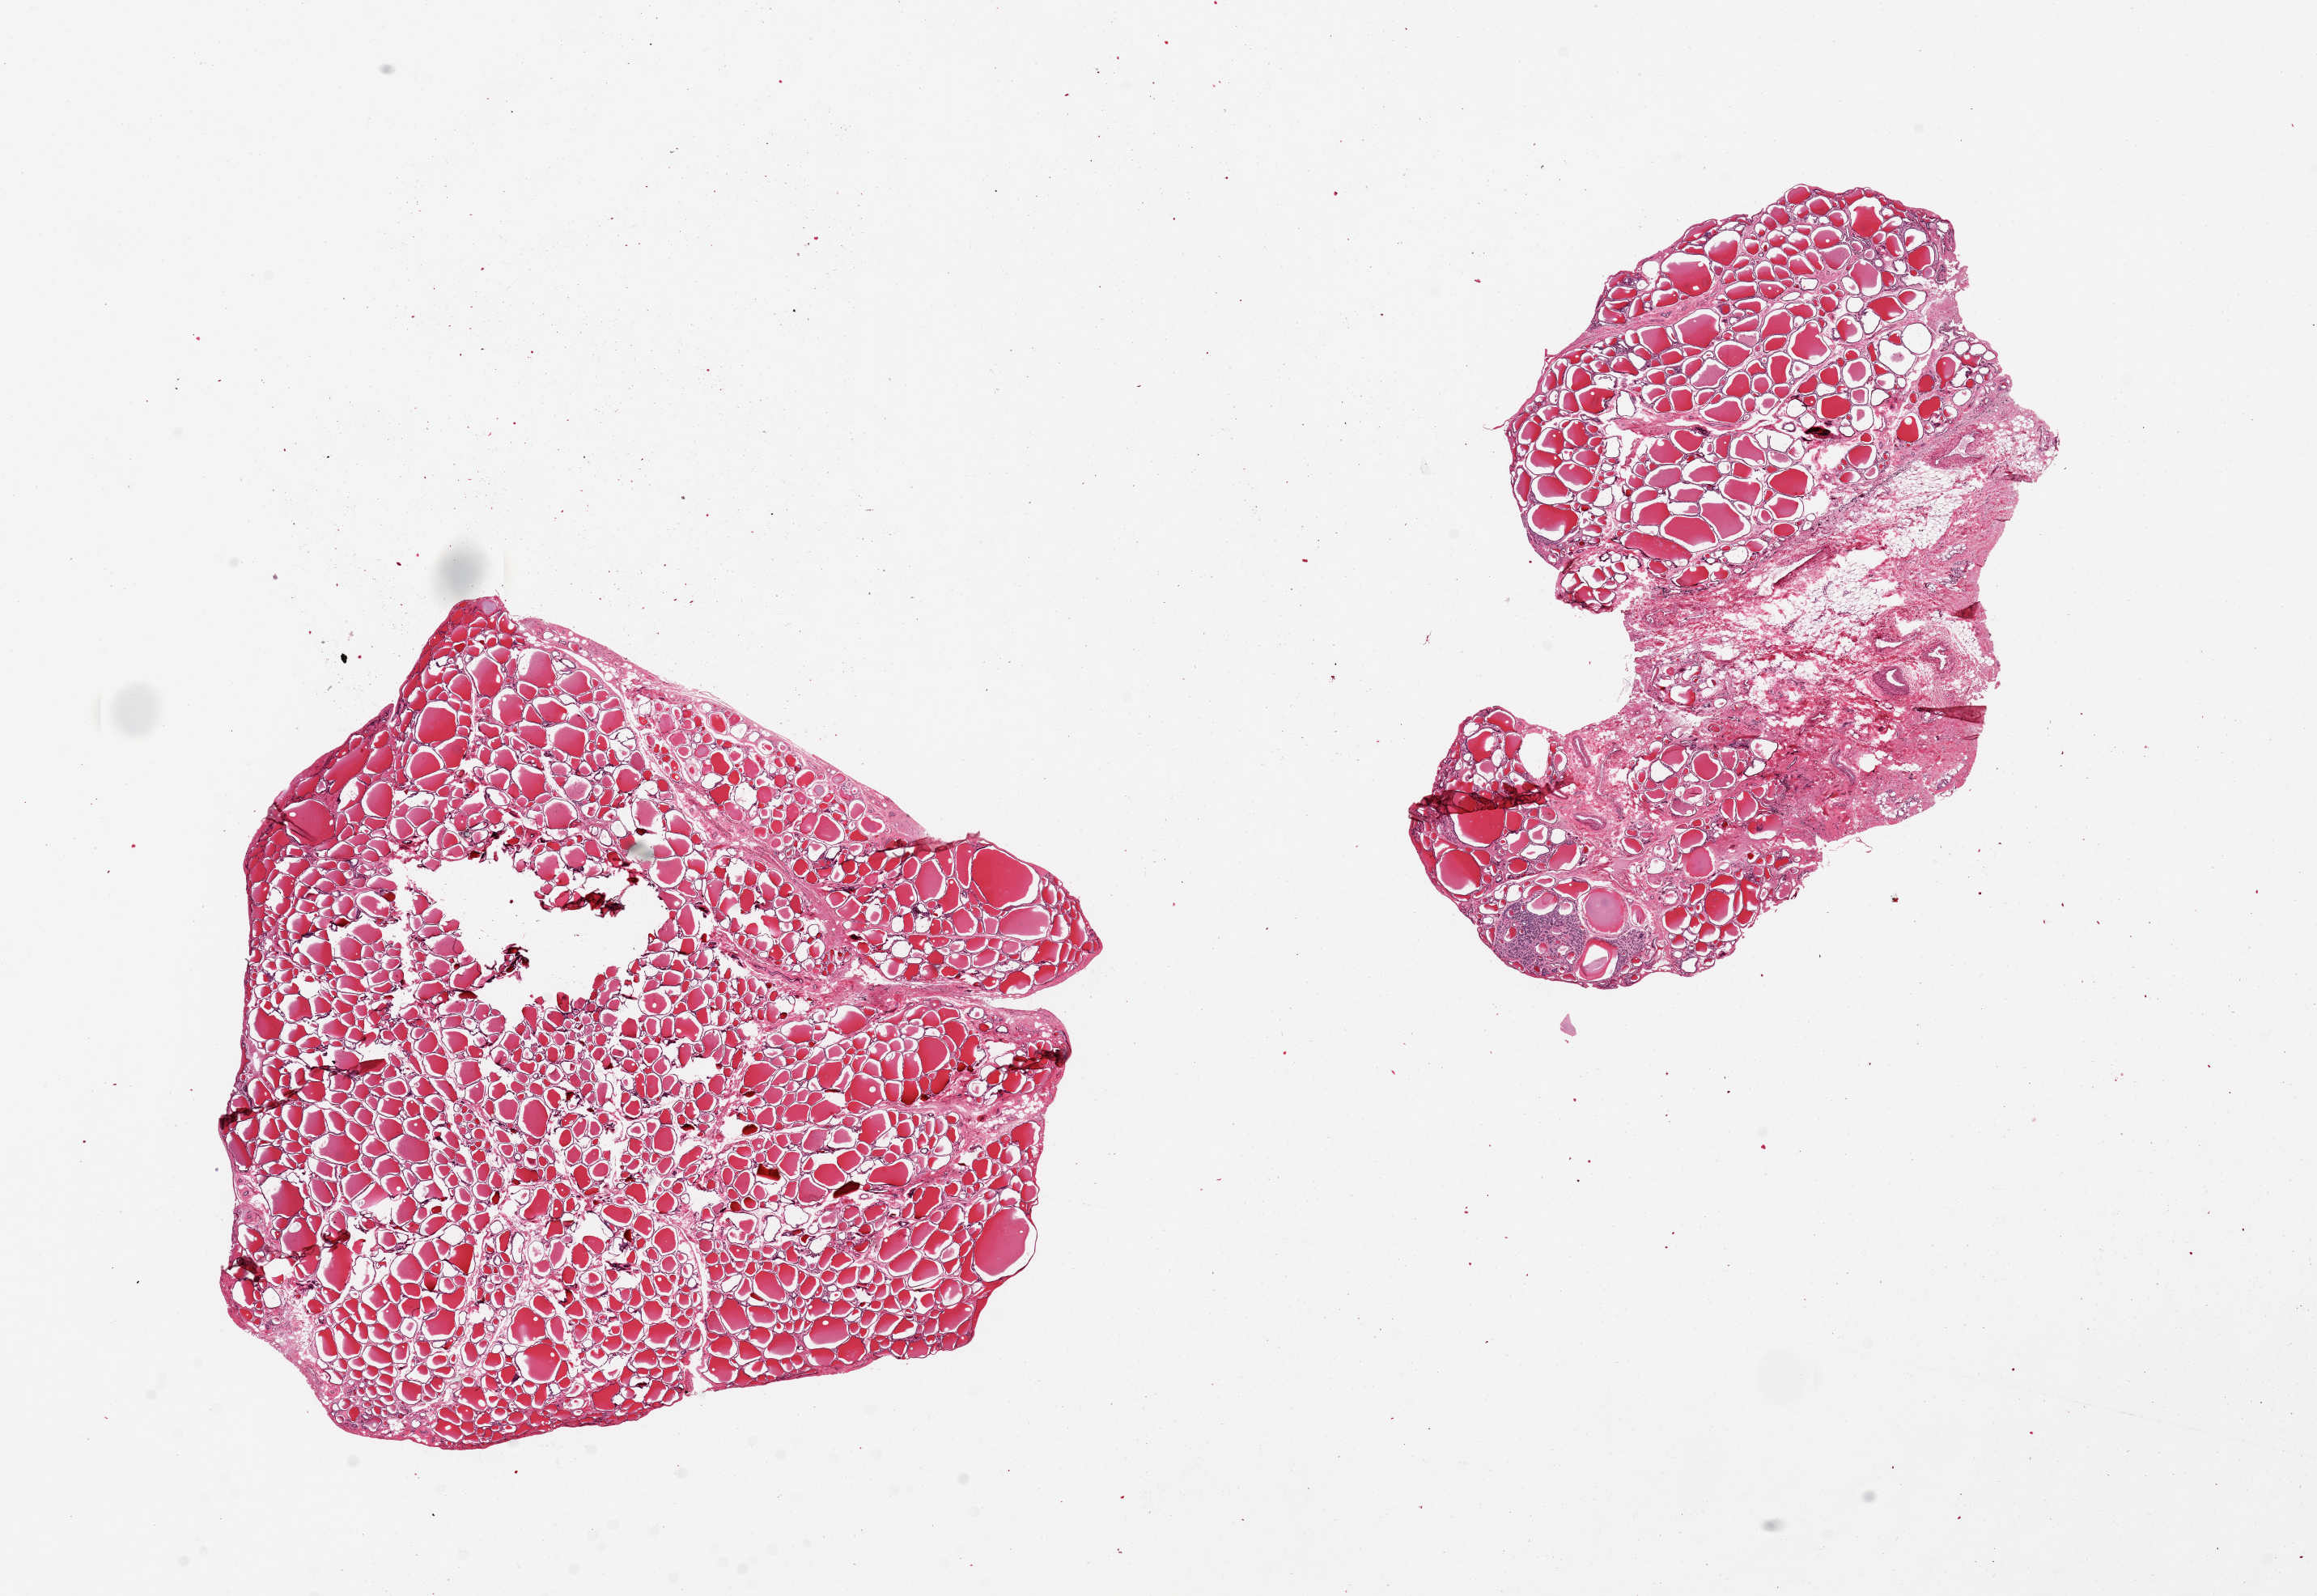
Whole-slide image, haematoxylin and eosin stain — shown as a low-resolution overview of the whole scanned area (about 22.6 x 15.6 mm, from a 20x scan), PAXgene-fixed paraffin-embedded (PFPE) section, target tissue: thyroid, tissue donor sample. Donor sex: male.
Reviewer comment on this tissue sample: 2 pieces, 8.5x8.5 & 8.5x6mm; small adenoma.